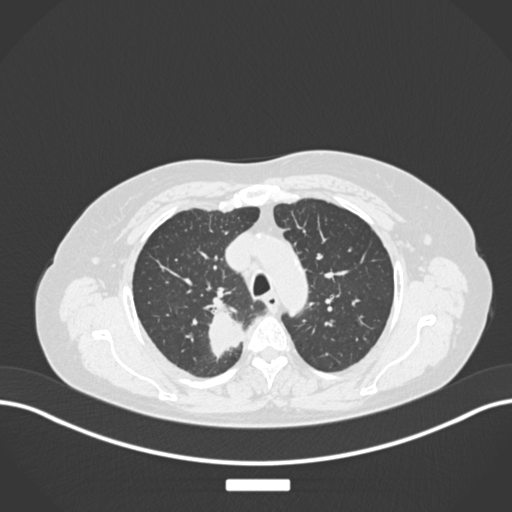
Chest CT, one axial slice. Position 193 of 237 along the scan axis. 120 kVp. Lung window (W 1500 / L -600 HU). 1 mm slice thickness. 512 × 512 image matrix, field of view 400 × 400 mm. Patient: female, 62 years. Case-level facts recorded for this patient, not image findings: clinical TNM (as recorded): T1c N1 M0.
Annotated regions visible in this slice (bounding box drawn by a radiologist):
- lung tumour (recorded histology: squamous cell carcinoma): bounding box <200,303,255,360> (left, top, right, bottom; pixels)